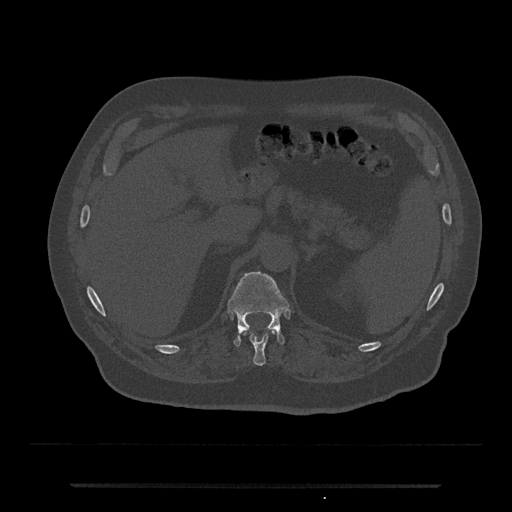
CT including the spine, one axial slice. Position 615 of 797 along the scan axis. Reconstruction kernel Br40s/3. Bone window (W 1800 / L 400 HU). 512 × 512 image matrix, field of view 434 × 434 mm. Patient: male, 80 years. Case-level facts recorded for this patient, not image findings: primary cancer: prostate.
Structures marked on this image (semi-automatic segmentation, software-assisted and operator-edited):
- T11 vertebra: box from (x=250, y=331) to (x=274, y=366) px
- T12 vertebra: (x=228, y=271)–(x=289, y=346)